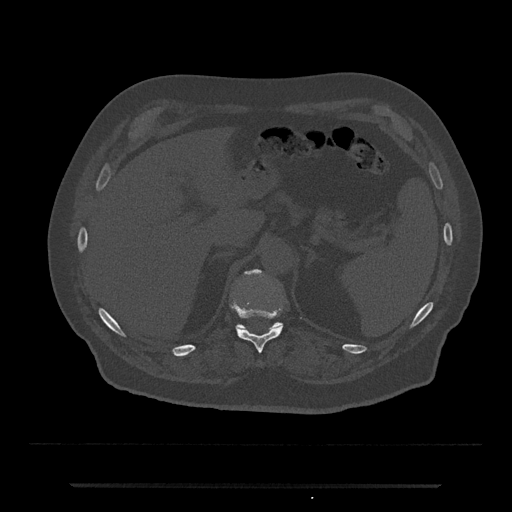
CT including the spine, one axial slice. Position 636 of 797 along the scan axis. Bone window (W 1800 / L 400 HU). 0.5 mm slice thickness. 512 × 512 image matrix, field of view 434 × 434 mm. Male patient, age 80 years. From the clinical record (not read from this slice): primary cancer: prostate; vertebrae with lytic lesions (as recorded): L1, T11.
Outlined on this slice (semi-automatically segmented with operator editing):
- T11 vertebra: box from (x=232, y=305) to (x=283, y=353) px
- T12 vertebra: (x=236, y=269)–(x=283, y=331)